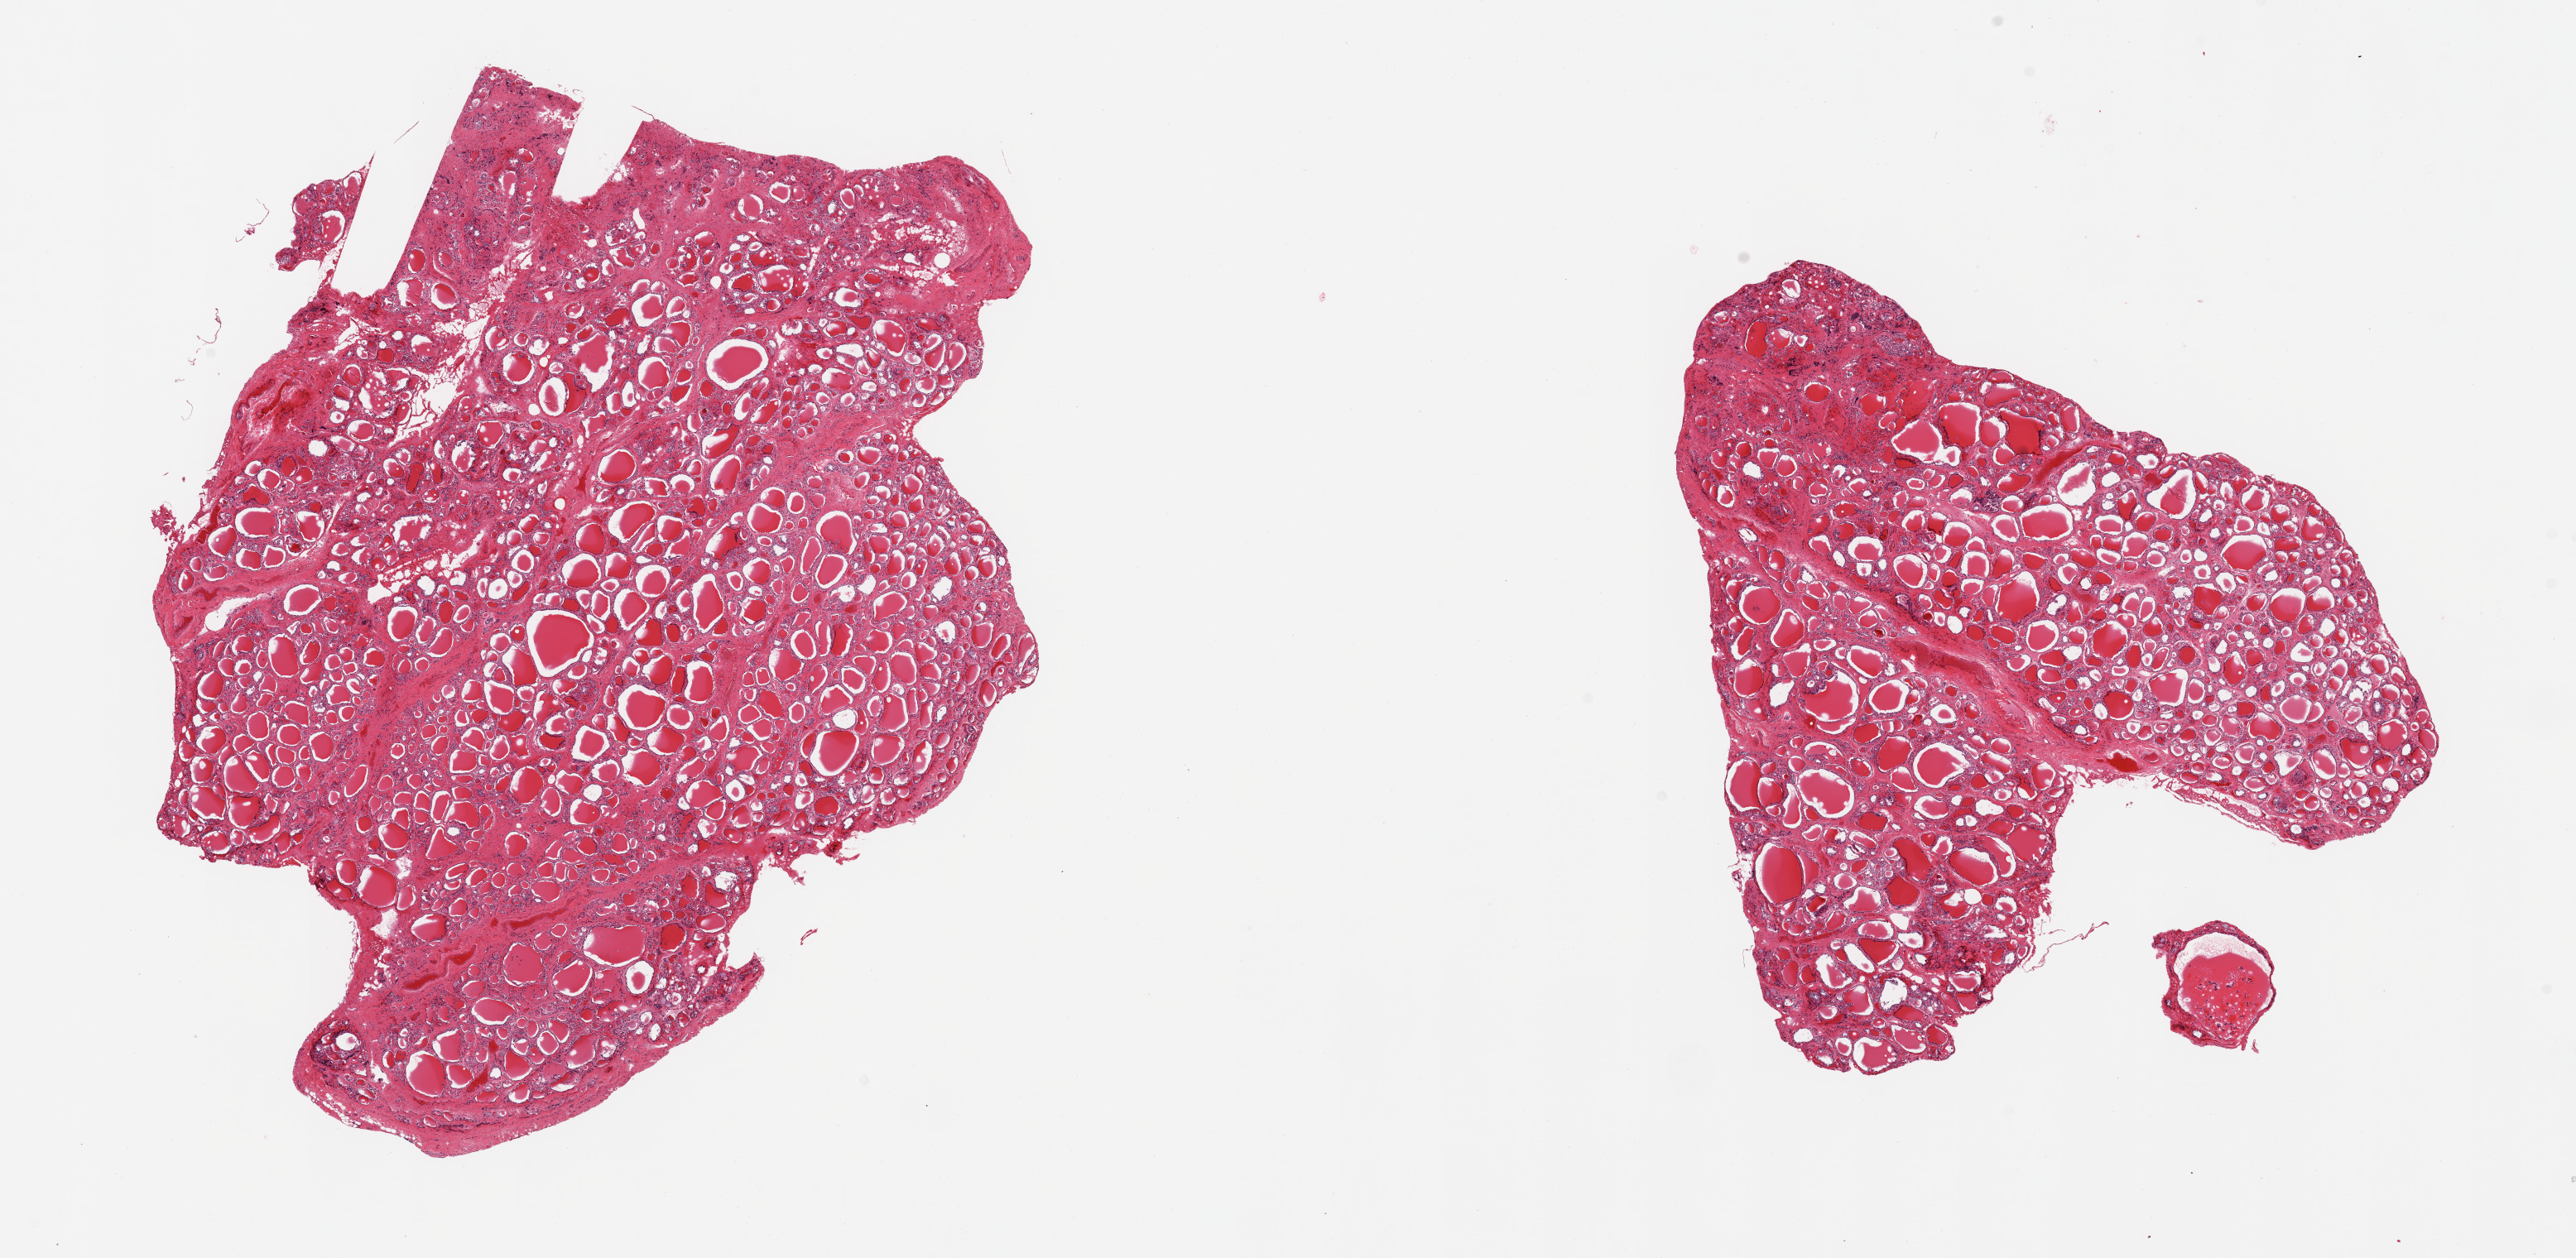
Haematoxylin and eosin whole-slide image, brightfield — low-resolution overview of the scanned area, about 24.6 x 12.0 mm (acquisition: 20x scan), PAXgene-fixed paraffin-embedded (PFPE) section, target tissue: thyroid, tissue donor sample. Donor: male.
Reviewer comment on this tissue sample: 2 pieces; mild interstitial fibrosis.